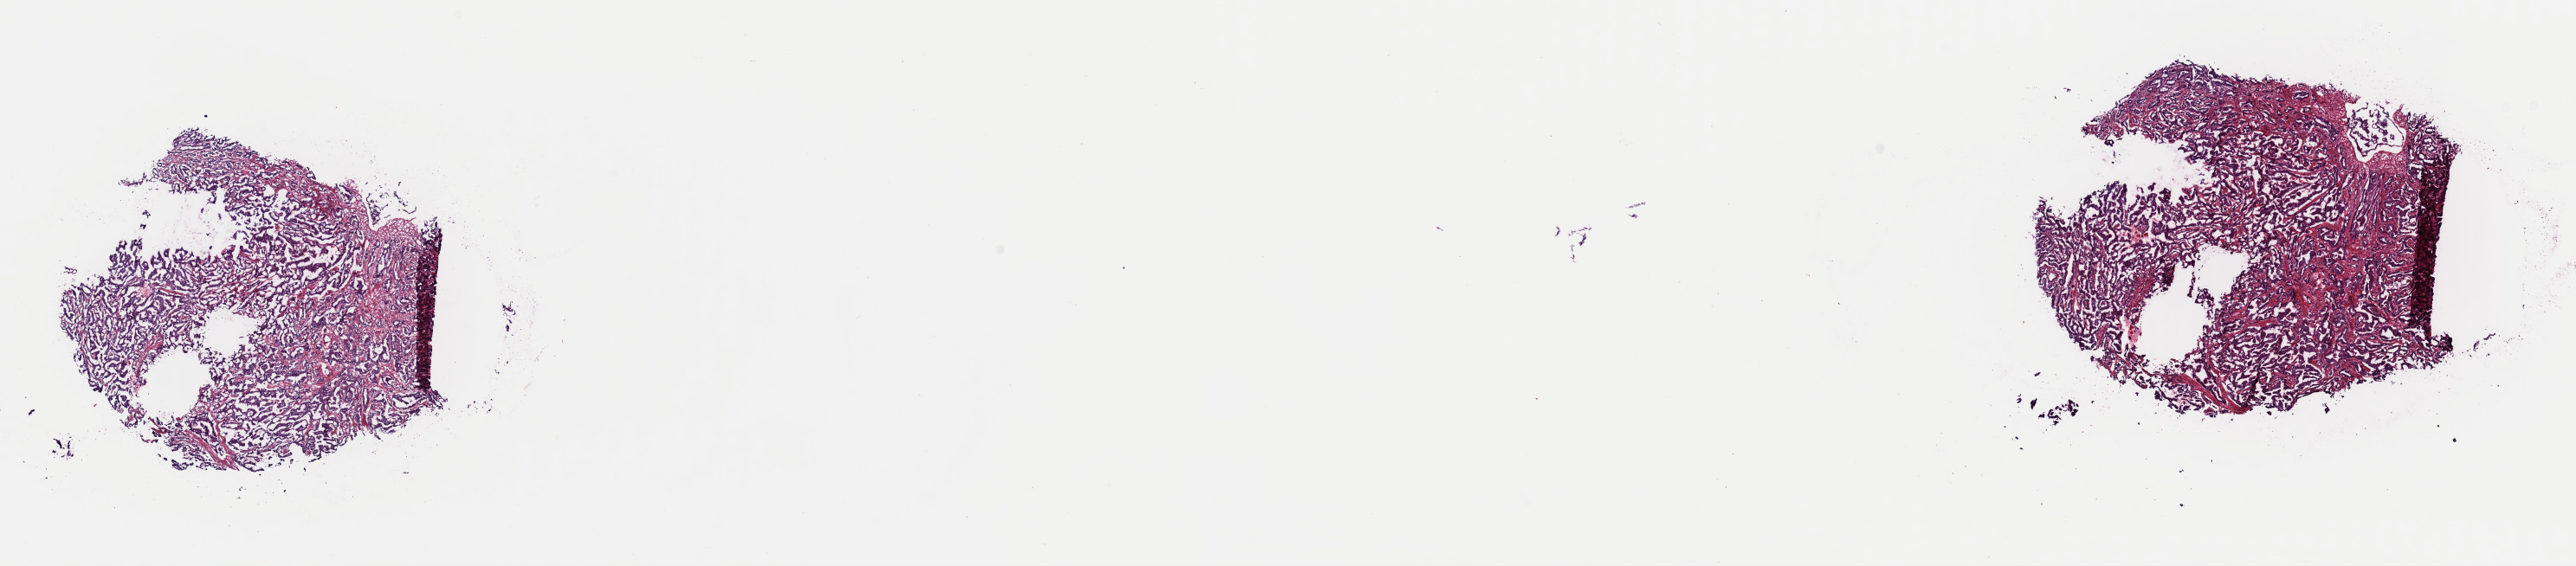
Whole-slide histology image, Hematoxylin and eosin (H&E) stained, low-resolution overview of the scanned area, about 23.5 x 5.2 mm. Frozen section. Primary tumour sample from the prostate. Male patient; age at initial diagnosis 62 years. Gleason score: 7 (4+3). Composition of this section per pathologist review: tumour cells 75%, tumour nuclei 75%, normal cells 0%, stromal cells 25%, necrosis 0%. Infiltration values recorded for this section: lymphocyte infiltration 3%, monocyte infiltration 0%, neutrophil infiltration 0%.
* histologic diagnosis: Adenocarcinoma, NOS (prostate gland)
* lymph nodes positive (case pathology): 0 of 11 examined